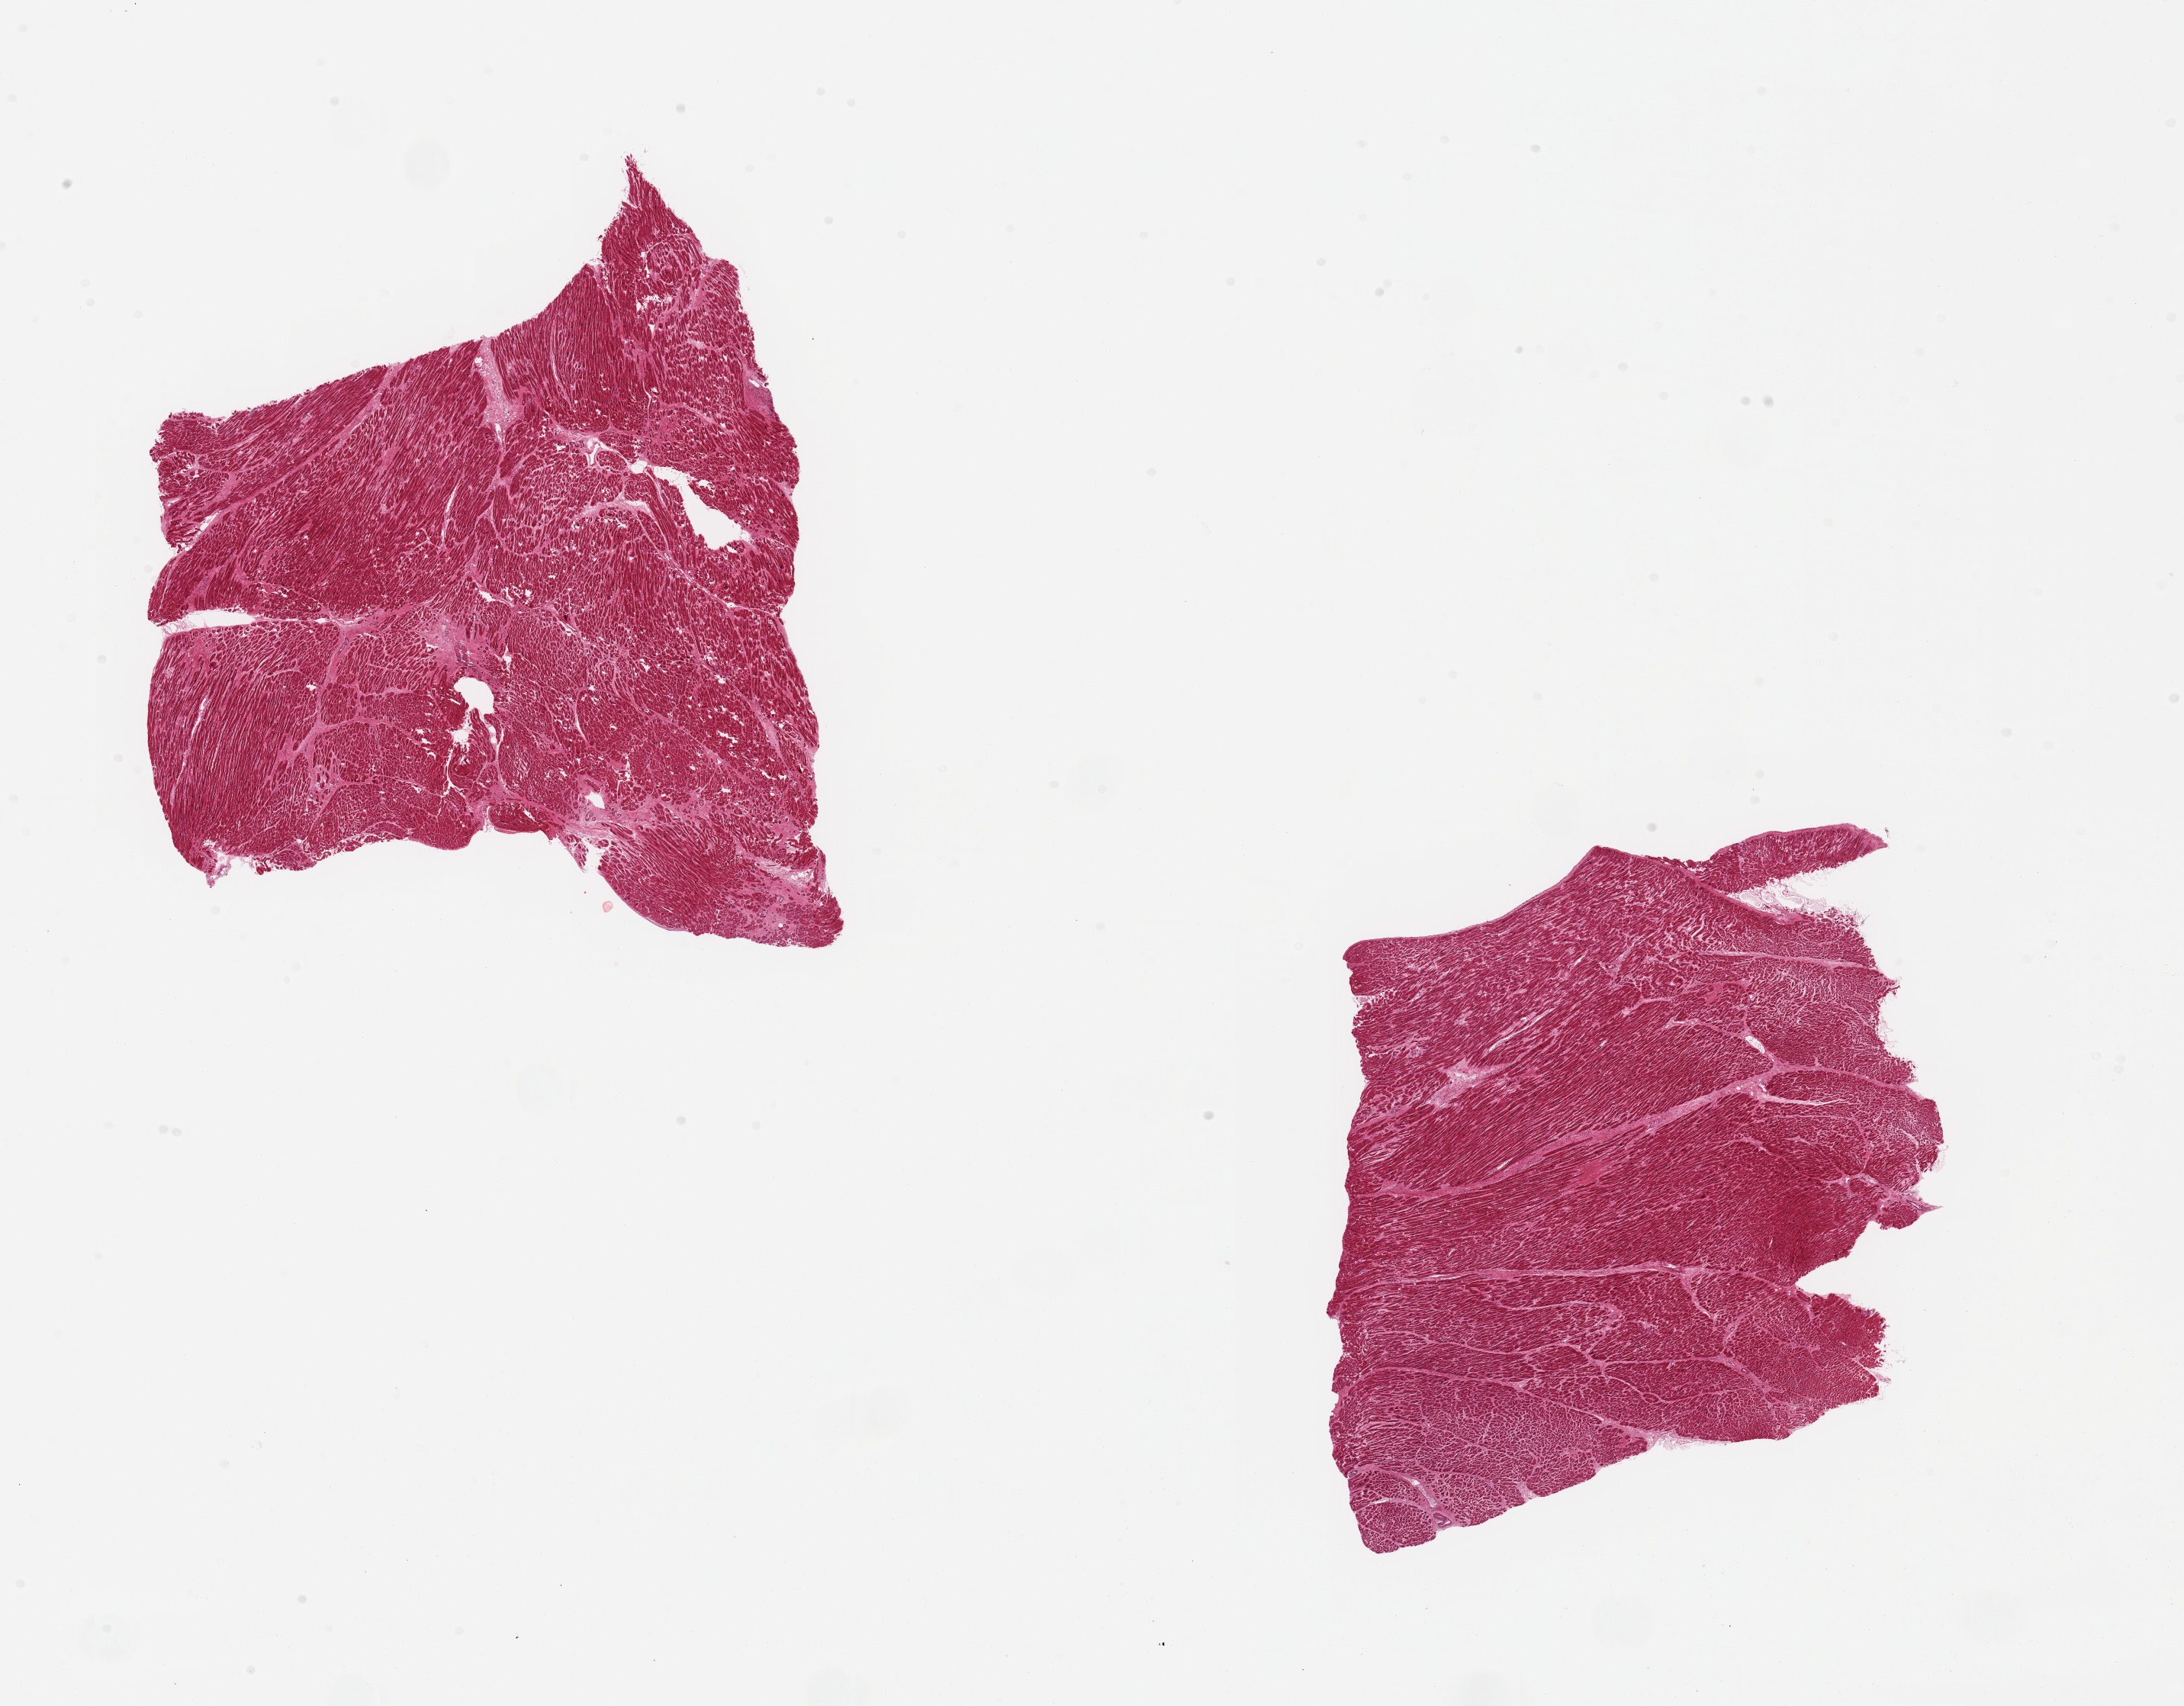
H&E whole-slide image, brightfield, whole scanned area (about 22.6 x 17.7 mm, from a 20x scan) shown as a low-resolution overview, PAXgene-fixed, paraffin-embedded tissue, sampled site (target tissue): heart, tissue donor sample. Donor: male.
• pathologist's review note for this sample: 2 pieces; some hypertrophy, interstitial and patchy fibrosis